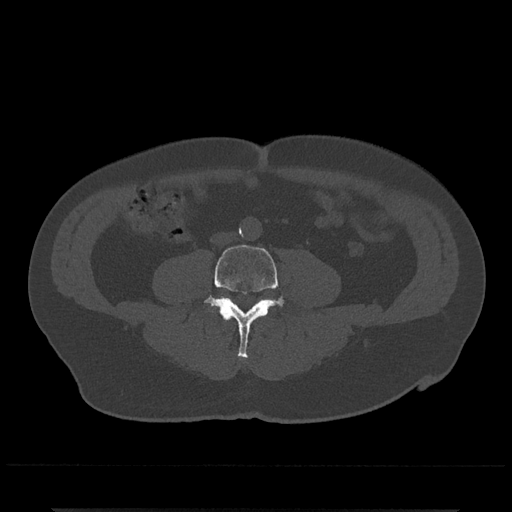
CT including the spine, one axial slice. 120 kVp. Bone window (W 1800 / L 400 HU). 0.5 mm slice thickness. 512 × 512 image matrix. Male patient, age 67 years. From the clinical record (not read from this slice): primary cancer: prostate.
Outlined on this slice (semi-automatic segmentation, software-assisted and operator-edited):
- L4 vertebra: bounding box [x1, y1, x2, y2] px = [204, 244, 284, 358]